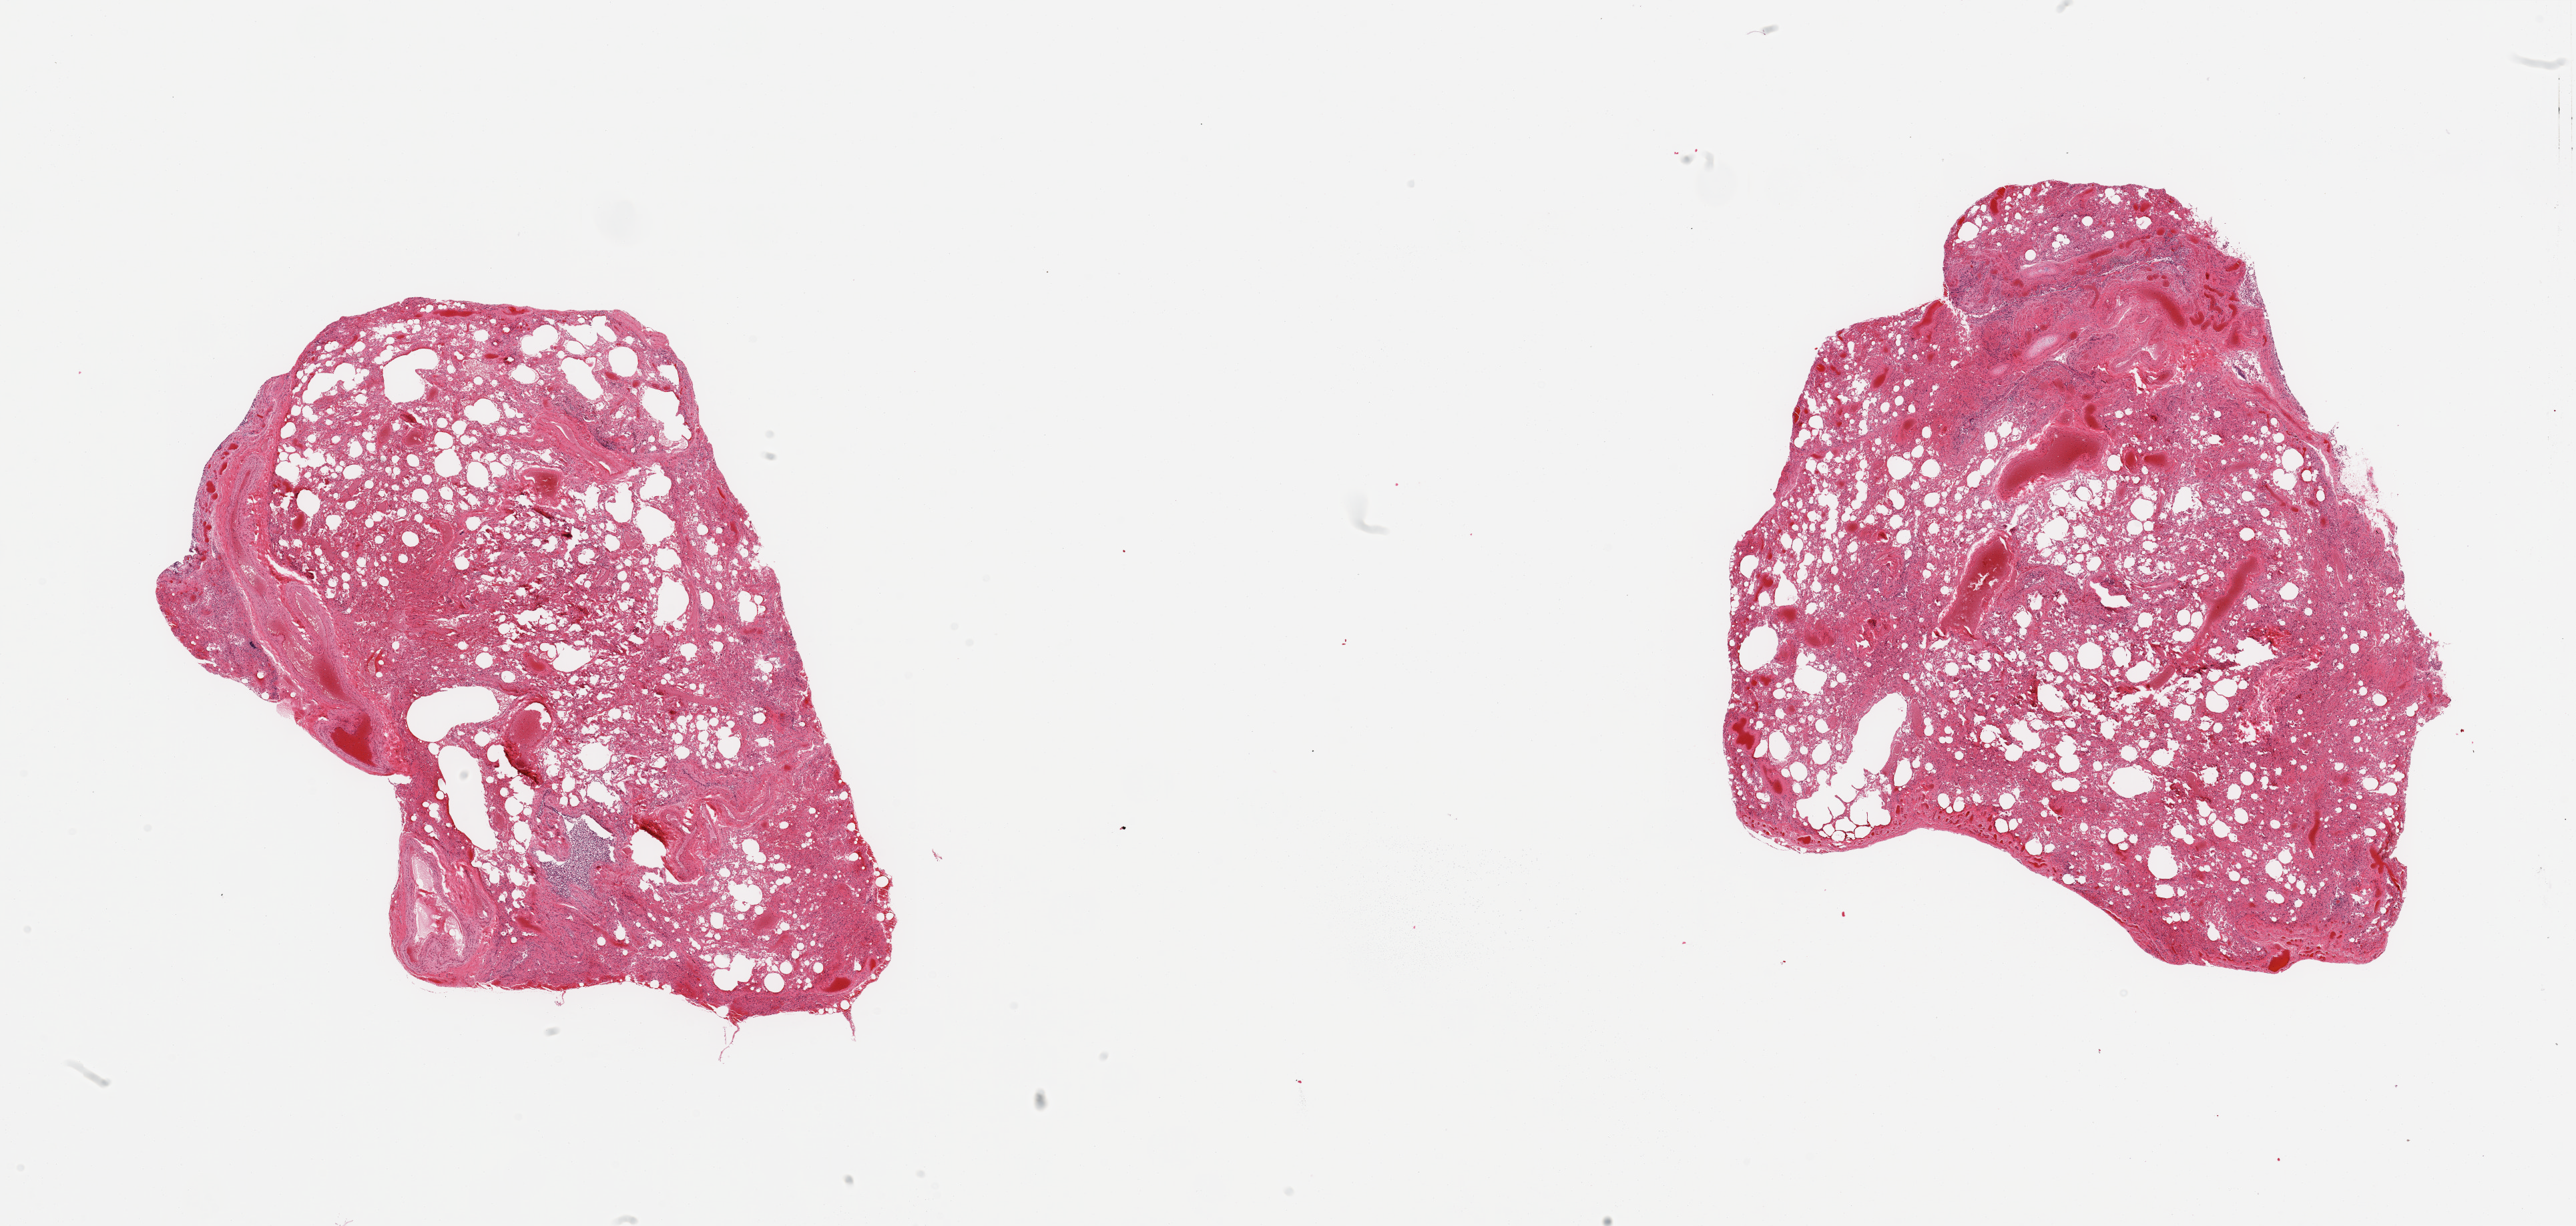
Digitized H&E-stained section, low-resolution overview of the scanned area, about 30.5 x 14.5 mm (acquisition: 20x scan), PAXgene-fixed, paraffin-embedded tissue, sampled site (target tissue): lung, tissue donor sample. Donor sex: male.
Pathologist's review note for this sample: 2 pieces; collapse and congestion, includes some larger vessels/cartilage, sloughed bronchial cells, one piece include pleura (target is 1cm below pleura).